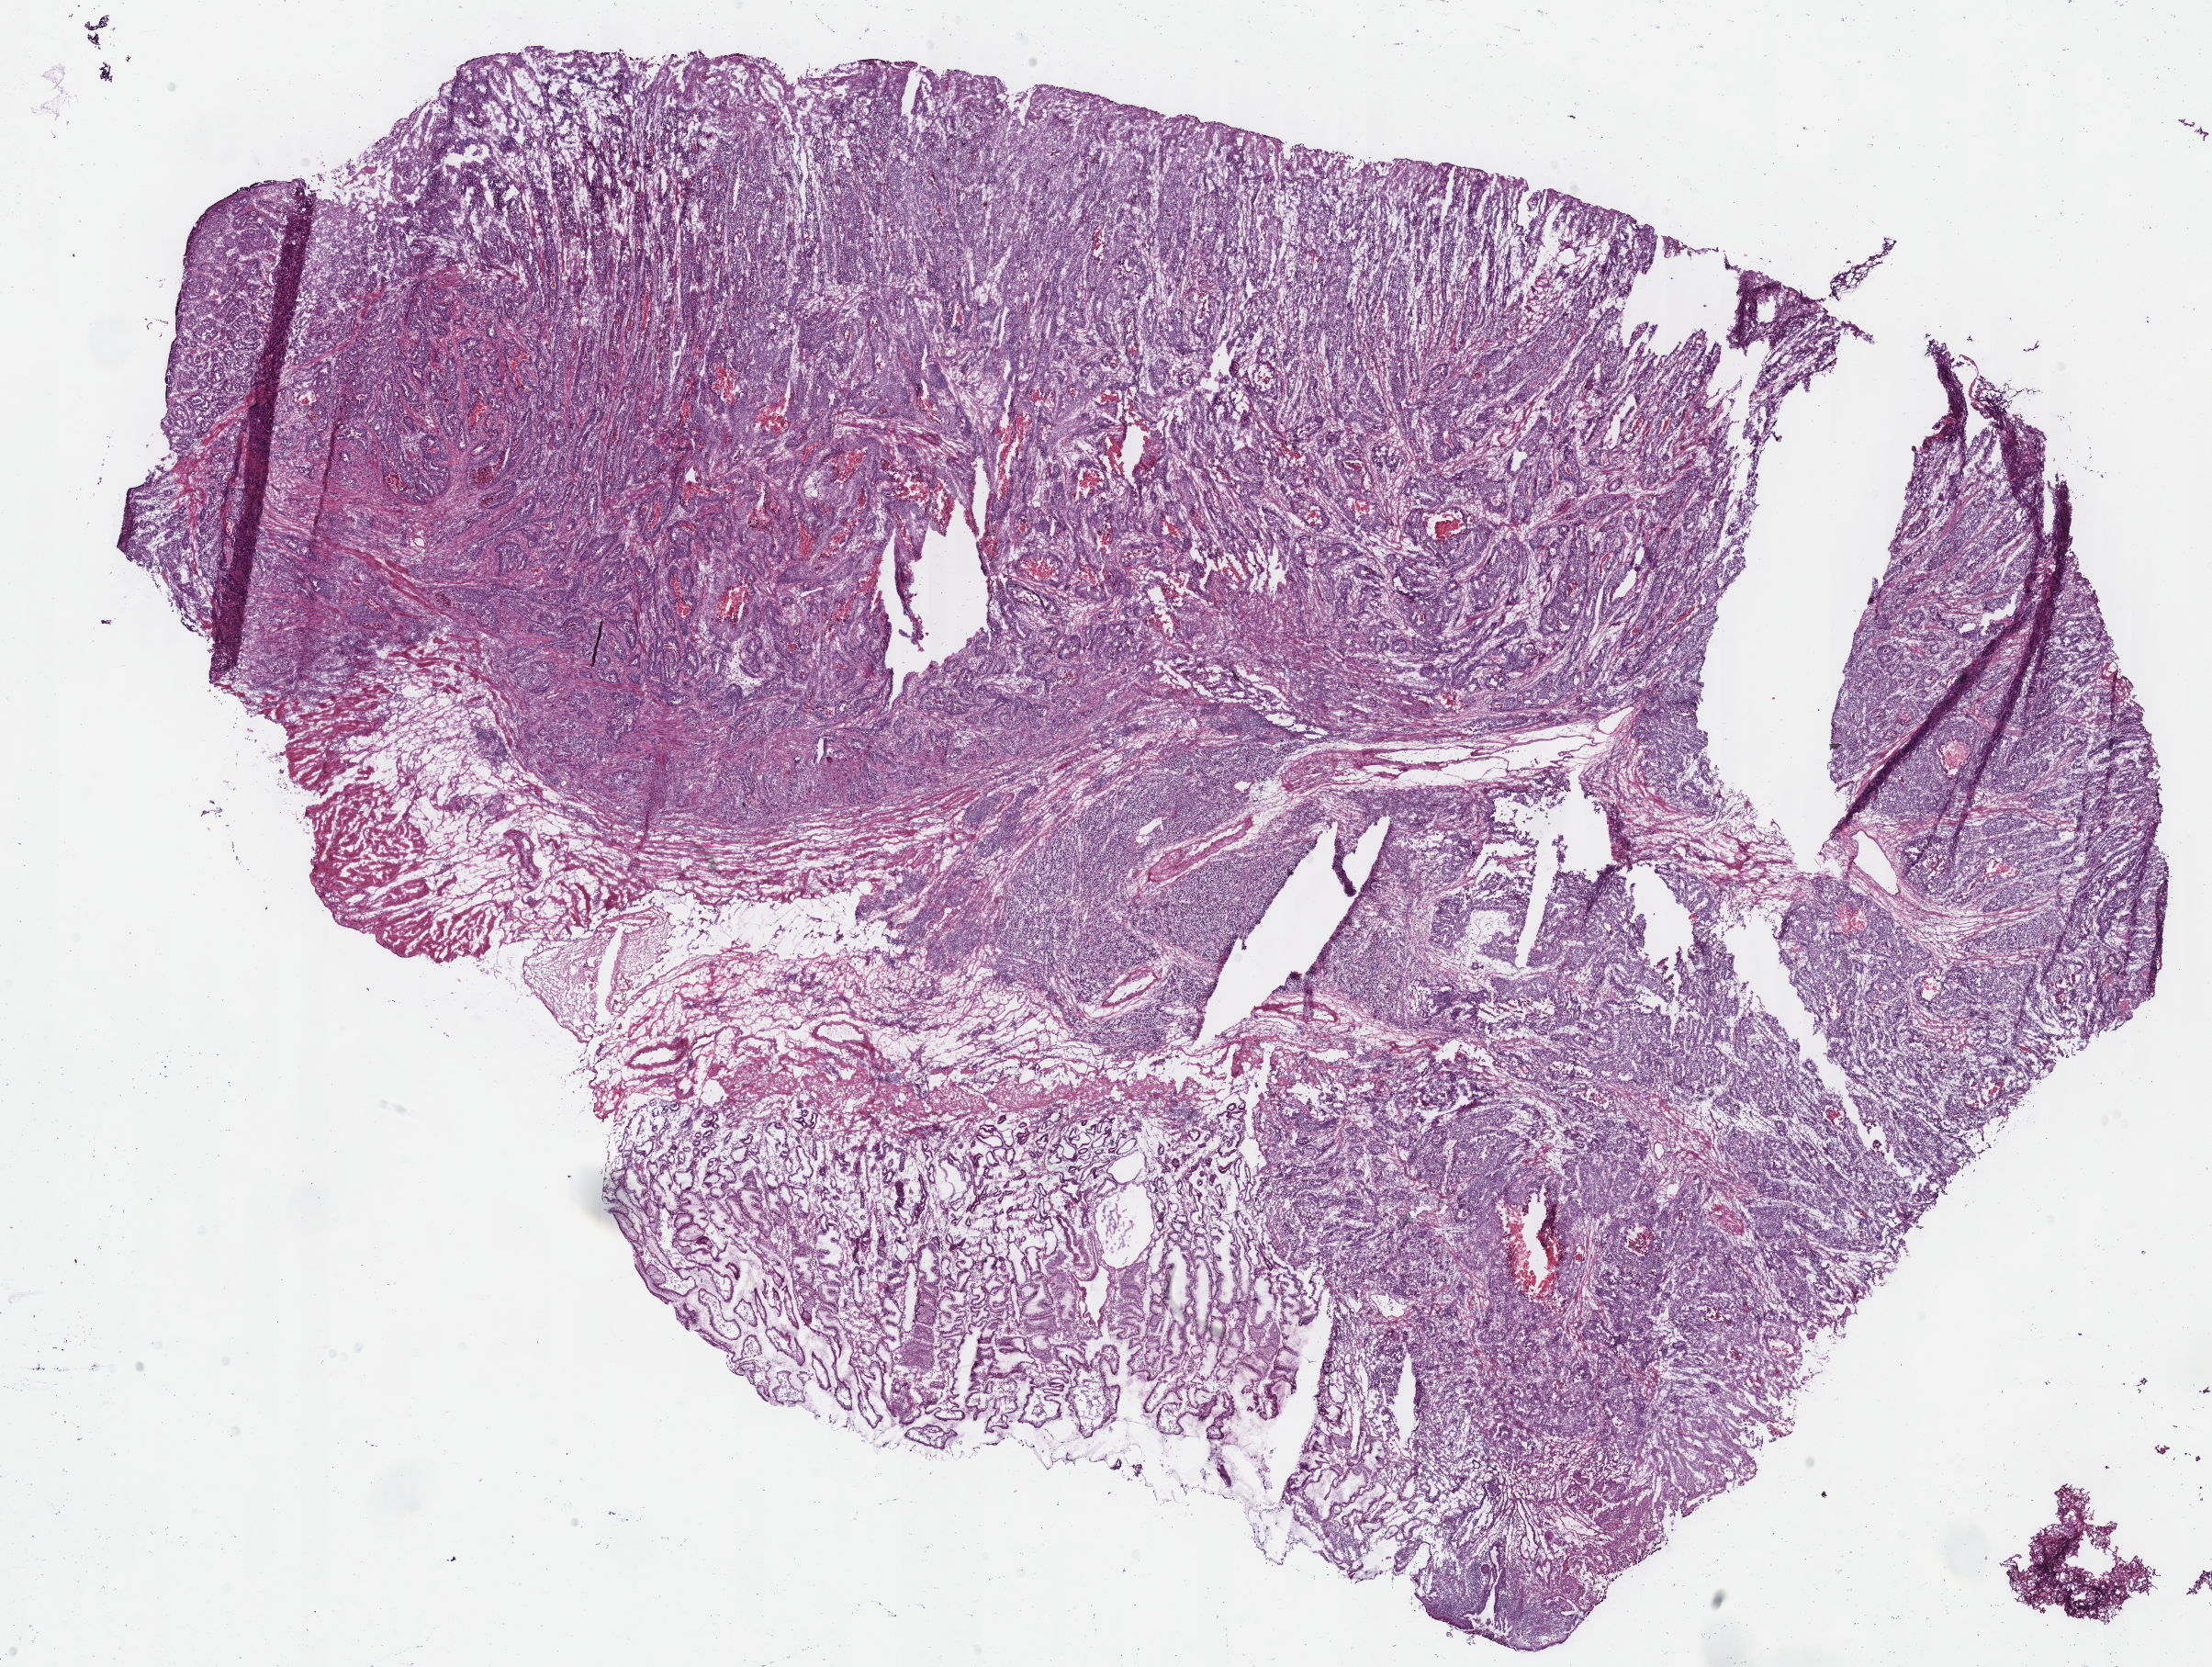
Hematoxylin and eosin (H&E) stained whole-slide image, shown as a low-resolution overview of the whole scanned area (about 19.0 x 14.3 mm, from a 40x scan). Frozen section. Sample: primary tumour, stomach. Female, age 68 years at initial diagnosis. Histologic grade: G3 (poorly differentiated). Pathologist review of this section (percent, as recorded): tumour cells 65%, tumour nuclei 70%, normal cells 18%, stromal cells 10%, necrosis 7%. Inflammatory infiltration, as recorded: lymphocyte infiltration 20%.
AJCC pathologic stage: IIIC (7th edition). Lymph nodes positive (case pathology): 7 of 13 examined. TNM: T4 N3a M0. Diagnosis: Adenocarcinoma, NOS.